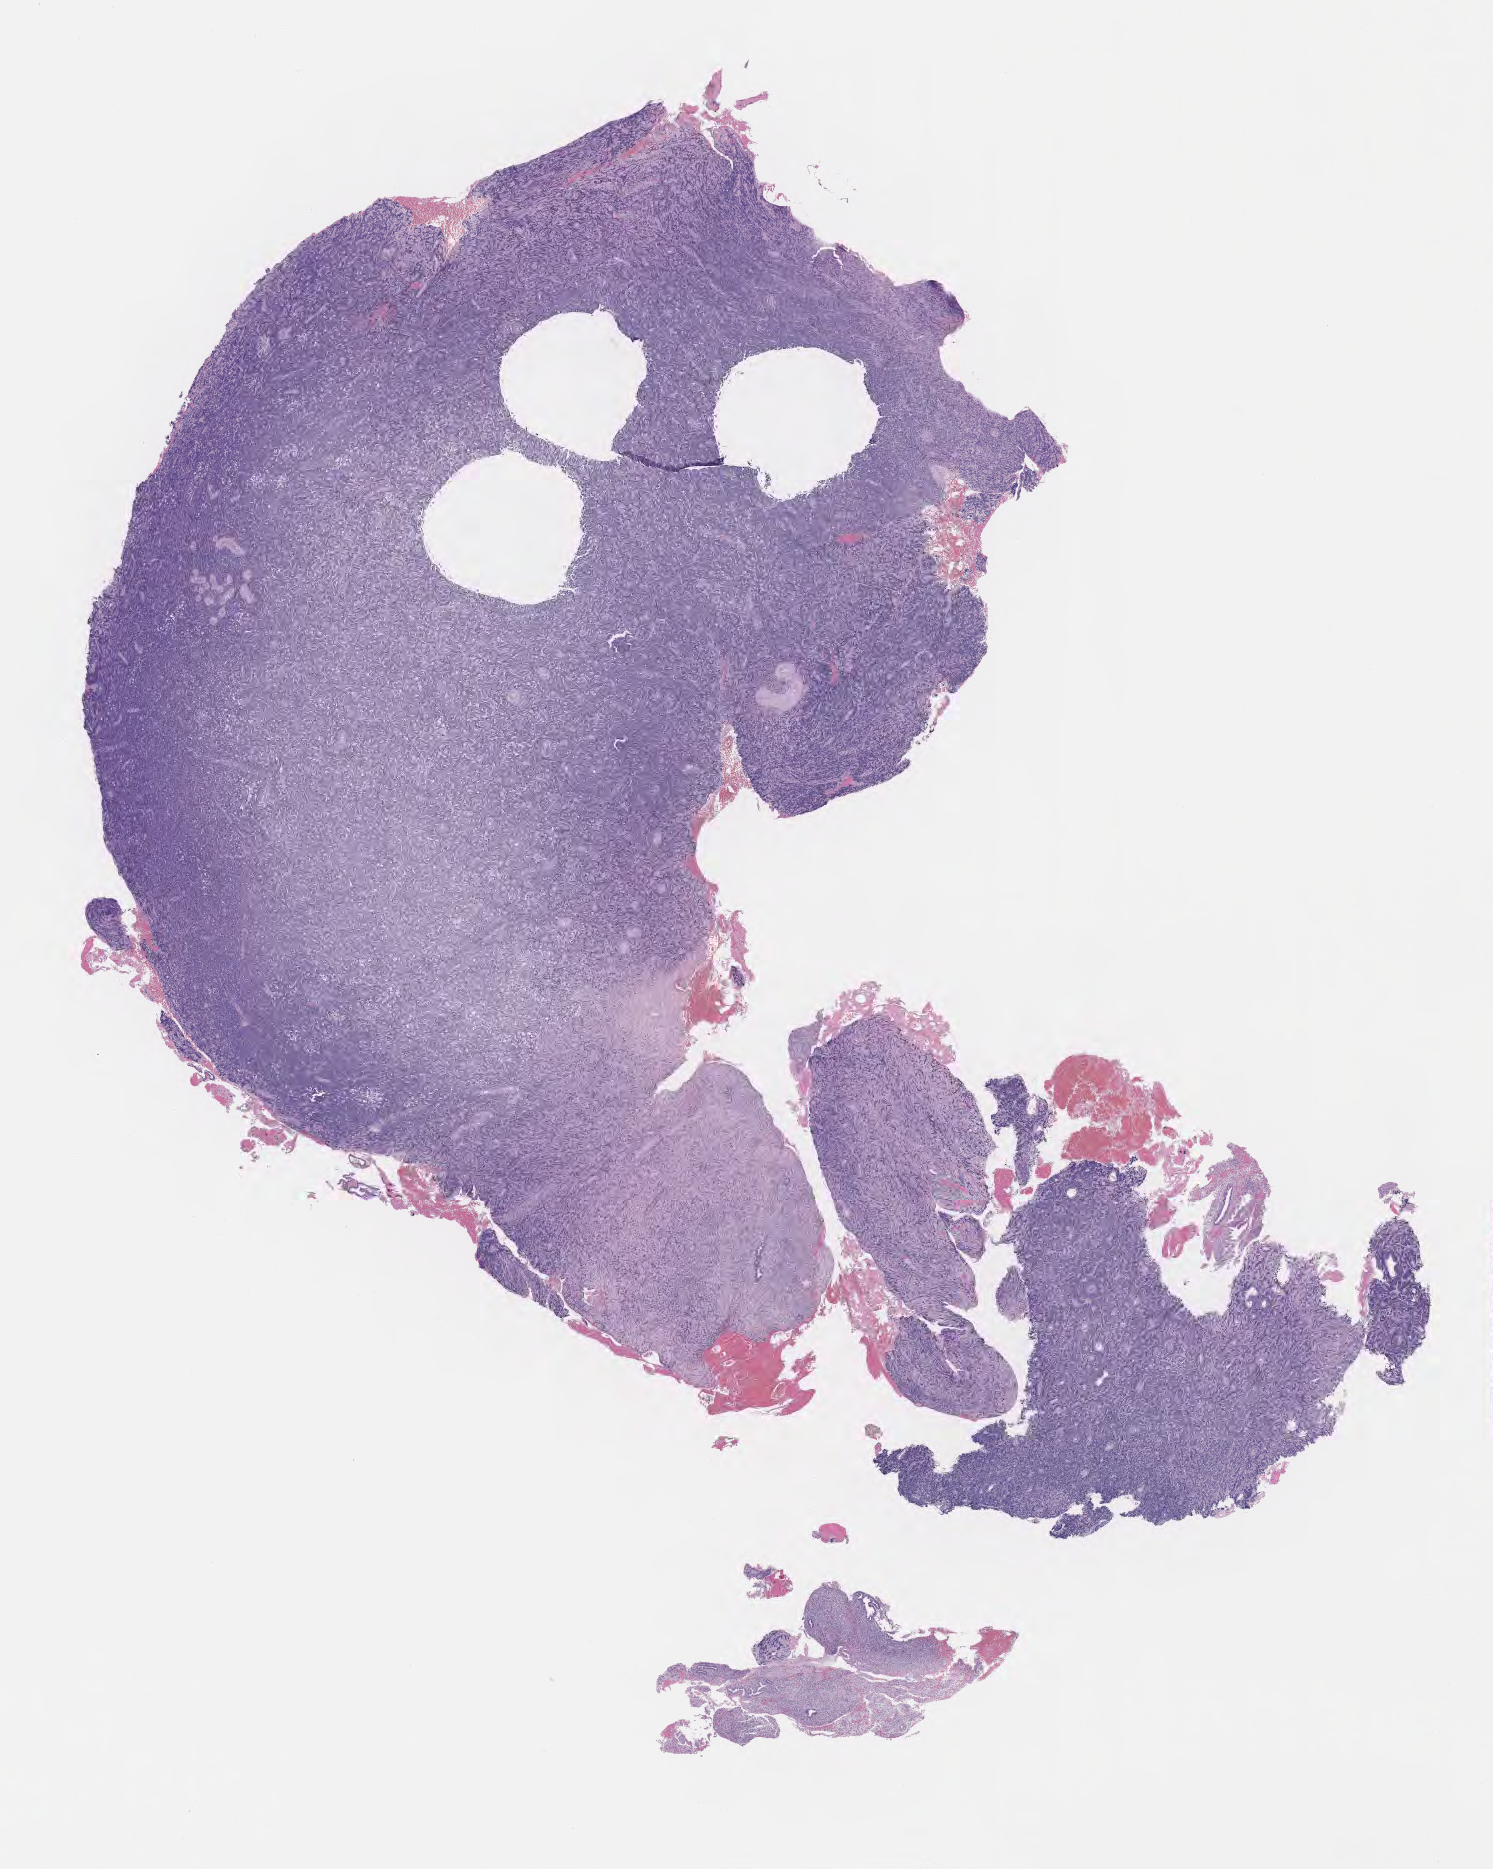
Digitized H&E-stained section — low-resolution overview of the scanned area, about 12.1 x 15.1 mm, specimen: tumor tissue, site: uterus. Patient female; aged 27.
Diagnosis: Burkitt lymphoma, NOS.